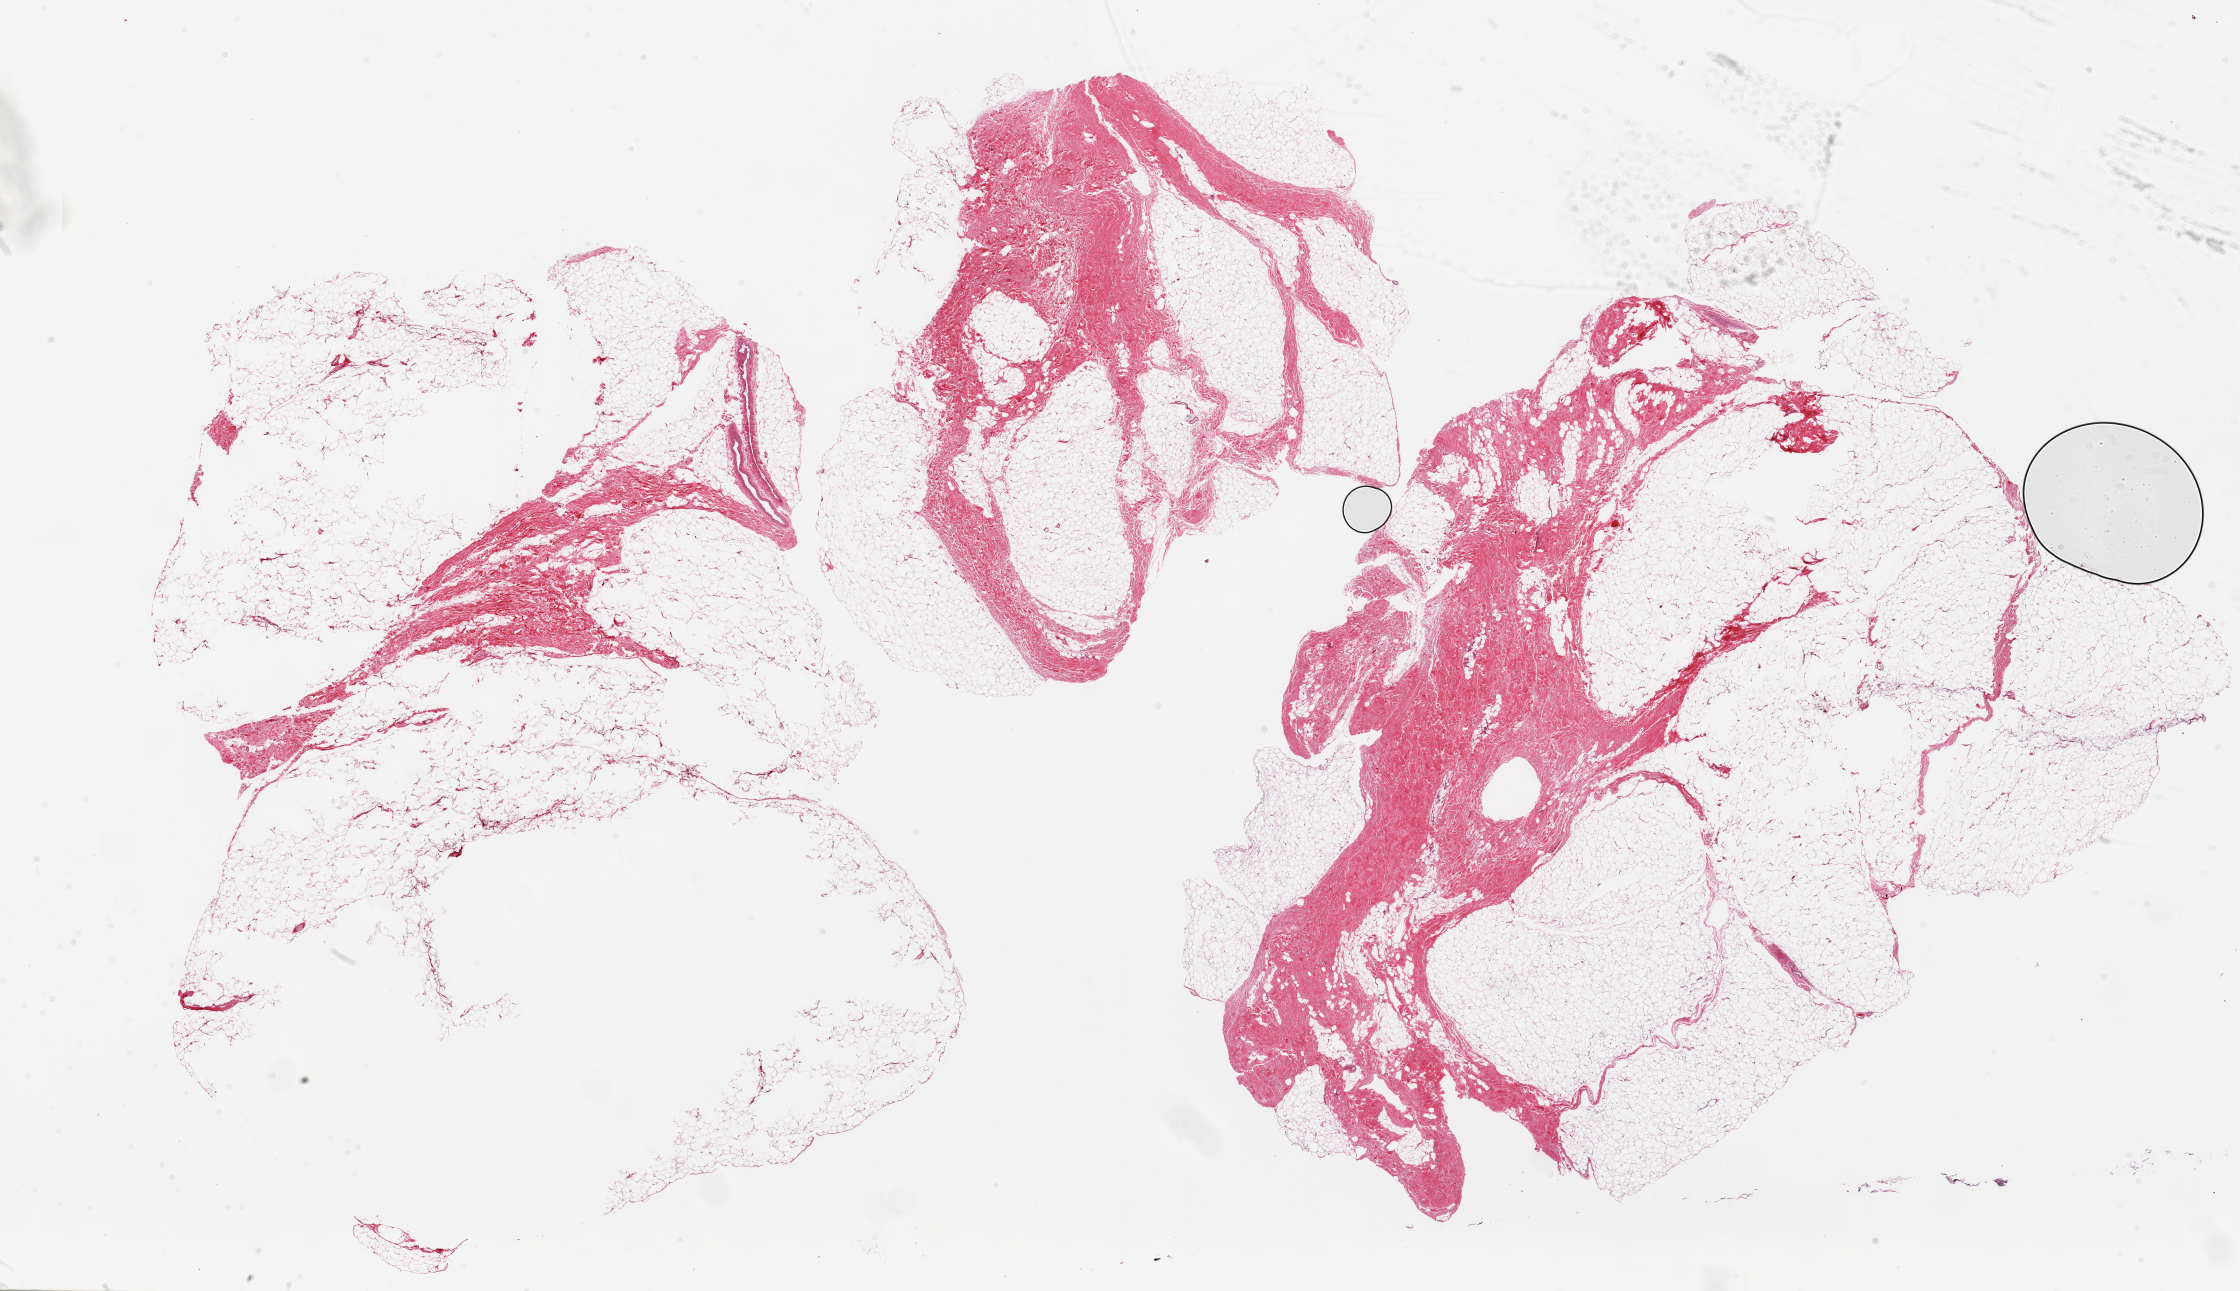
Digitized haematoxylin and eosin-stained section, brightfield, a low-resolution overview of the entire scanned area, about 35.4 x 20.4 mm (acquisition: 20x scan). PAXgene-fixed, paraffin-embedded tissue. Target tissue: breast. Donor tissue sample. Donor: male.
Pathologist's review note for this sample: 2 pieces, fibroadipose tissue, no ductal elements.